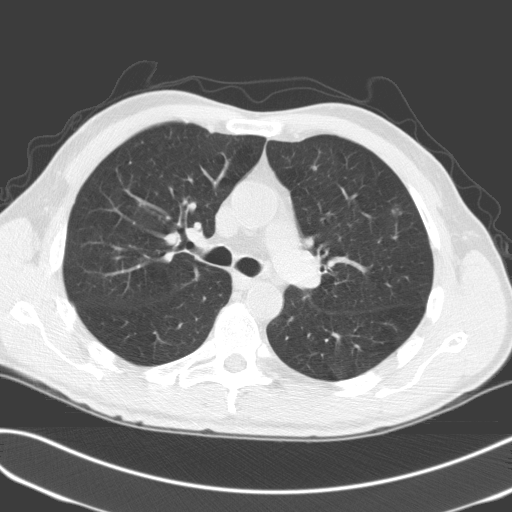
Chest CT (low-dose screening protocol), one axial image; third annual screen; lung window (W 1500 / L -600 HU); standard (soft-tissue) reconstruction kernel (C); 120 kVp; slice 64 of 170 in the series. Male, age 68 years at enrolment.
Lesion marked by an expert reader, bounding box <363,195,416,243> (left, top, right, bottom; pixels). Reader record for this screening exam (exam-level; its link to the box is not recorded): non-calcified nodule or mass ≥4 mm, left upper lobe, 9 × 7 mm, poorly defined margins, mixed attenuation, pre-existing on the prior screen: no. Official screen result: positive, other.